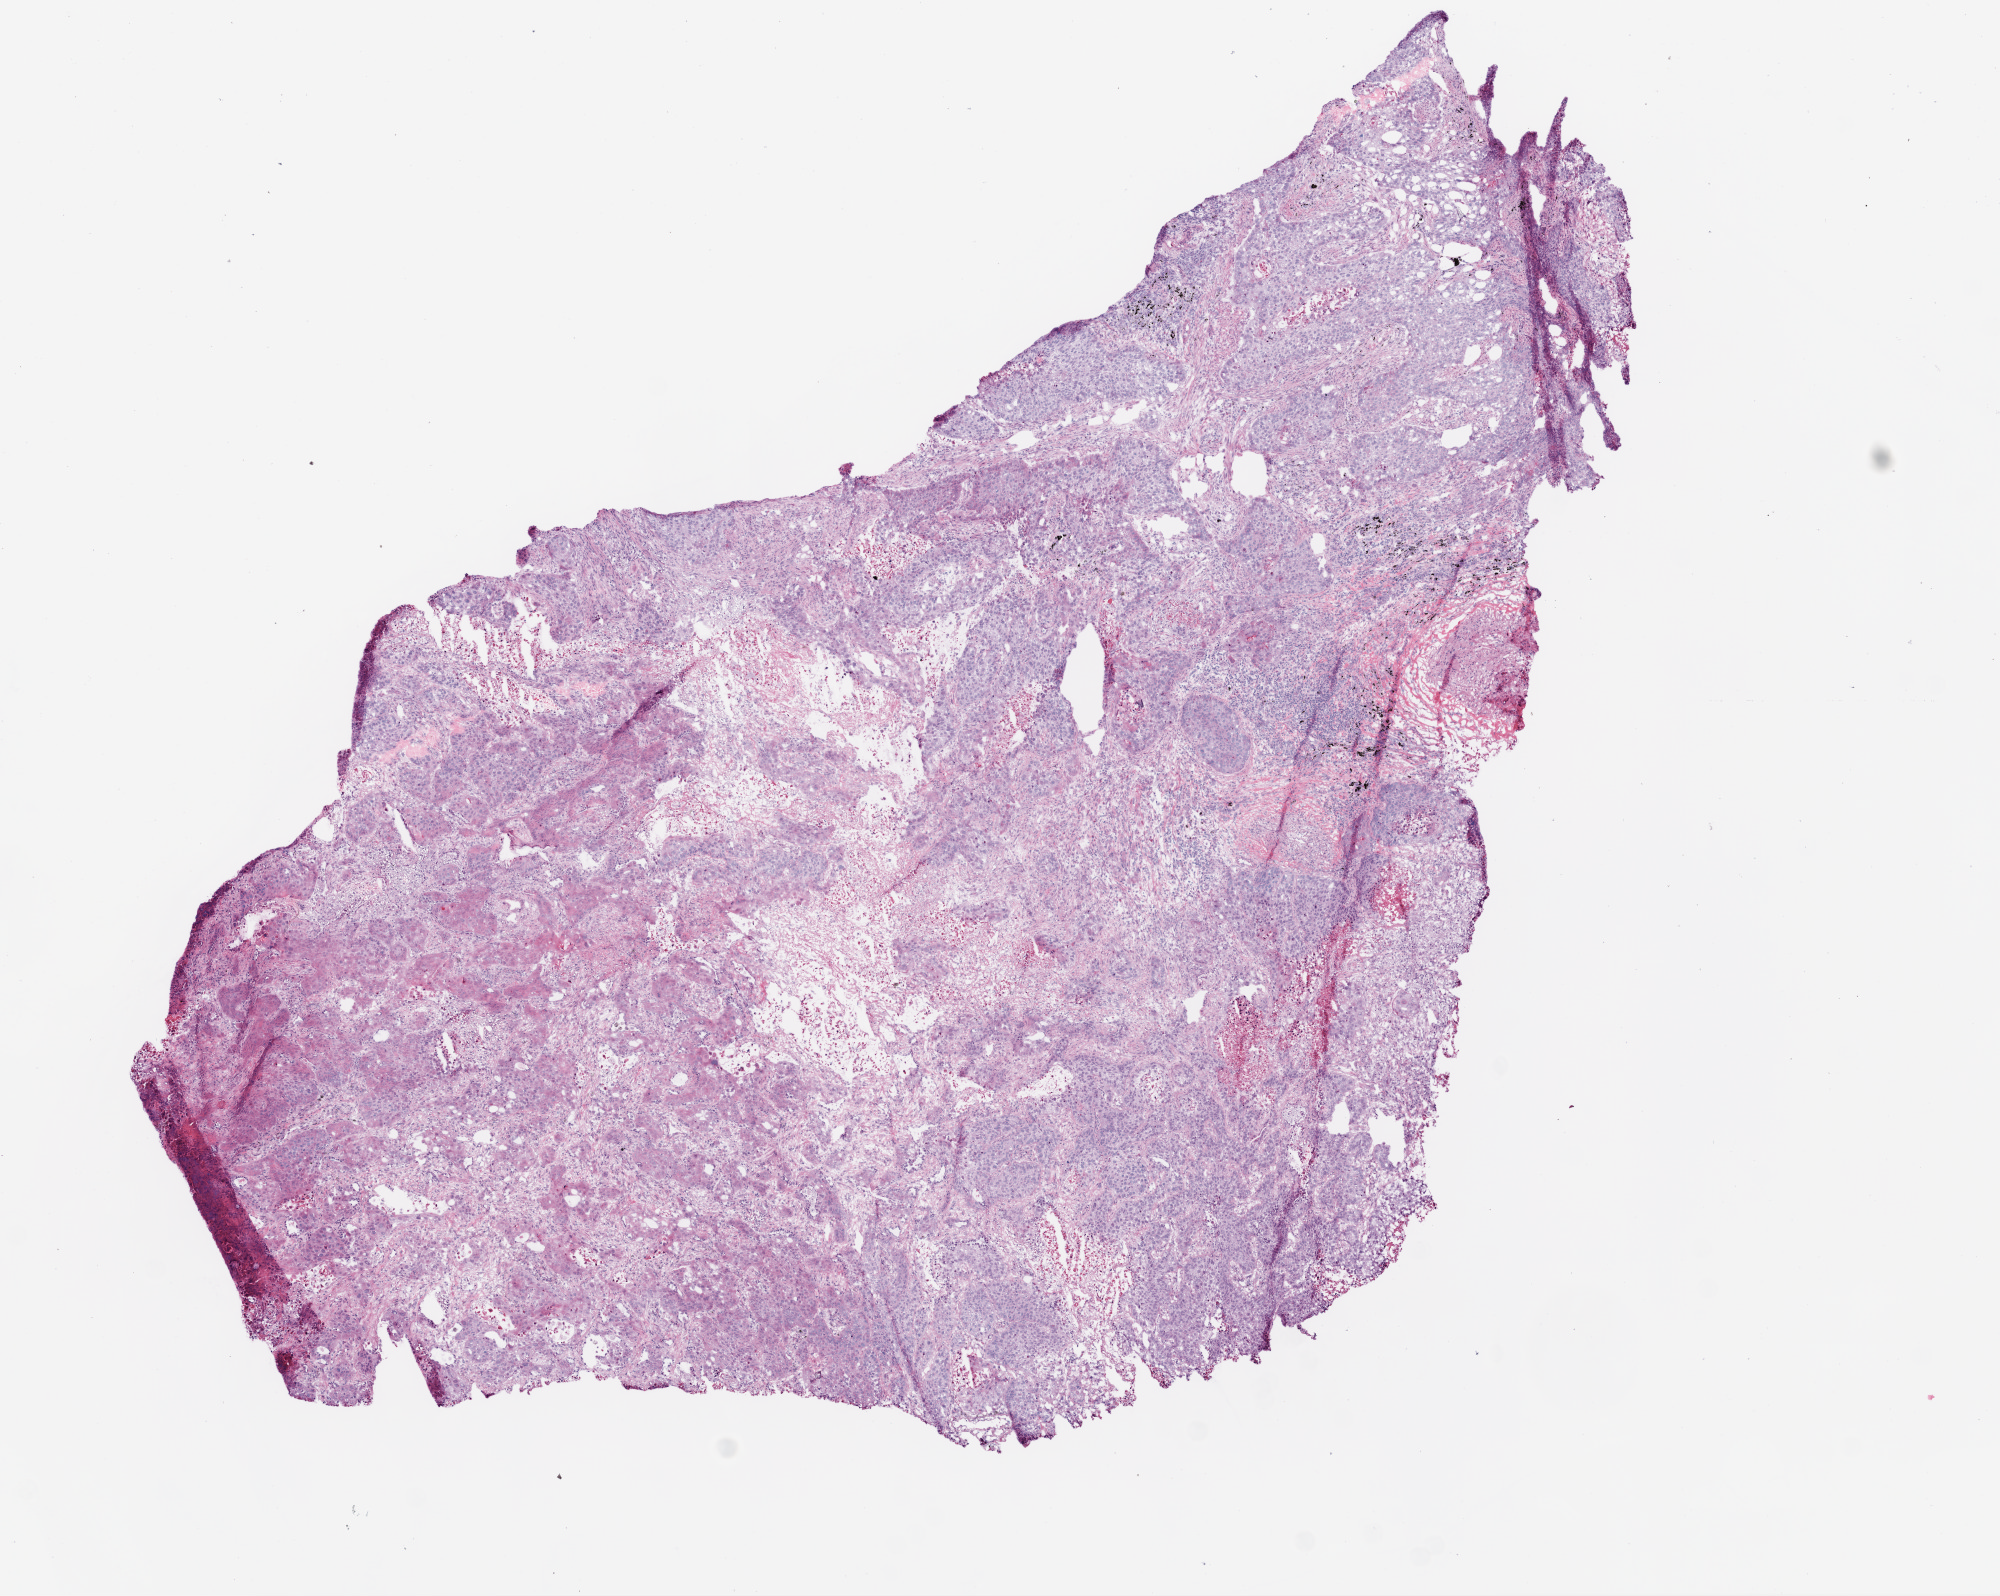
Whole-slide histology image, H&E-stained, whole scanned area (about 8.0 x 6.4 mm) shown as a low-resolution overview; frozen section from the top of the tissue portion; primary tumour sample from the lung. Male patient; age at initial diagnosis 52 years. Slide review estimates, as recorded: tumour cells 82%, tumour nuclei 80%, stromal cells 4%, necrosis 14%. Infiltration values recorded for this section: lymphocyte infiltration 1%.
Diagnosis: Squamous cell carcinoma, NOS (lower lobe, lung). TNM: T2a N0 M0. Laterality: left. AJCC pathologic stage: IB.